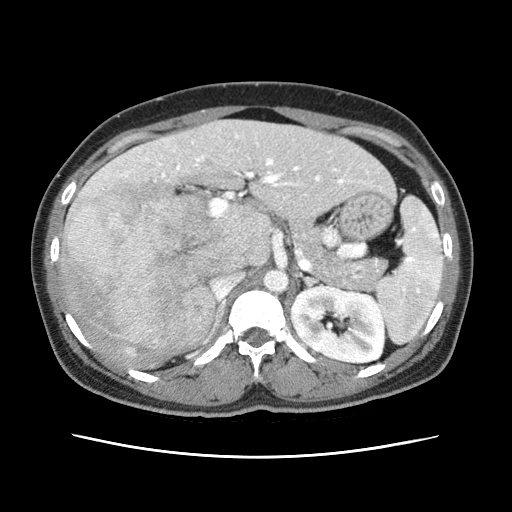
Contrast-enhanced abdominal CT (liver protocol), one axial slice; position 34 of 79 along the scan axis; 120 kVp; soft-tissue window (W 400 / L 40 HU); 2.5 mm slice thickness; 512 × 512 image matrix, field of view 340 × 340 mm. From the clinical record (not read from this slice): diagnosis: hepatocellular carcinoma (patient treated with transarterial chemoembolisation; whether this scan precedes or follows treatment is not stated here); TNM stage (as recorded): Stage-I; Child-Pugh class: A; tumour differentiation: moderately differentiated; tumour nodularity: uninodular.
Outlined on this slice (semi-automatically segmented with operator editing):
- abdominal aorta: bounding box (x1, y1, x2, y2) in pixels: (265, 269, 288, 292)
- liver parenchyma outside the tumour (the mass and vessels are separate outlines, so this box may not span the whole liver): (60, 119, 394, 368)
- mass: (59, 178, 224, 368)
- liver vessels: (121, 135, 344, 187)